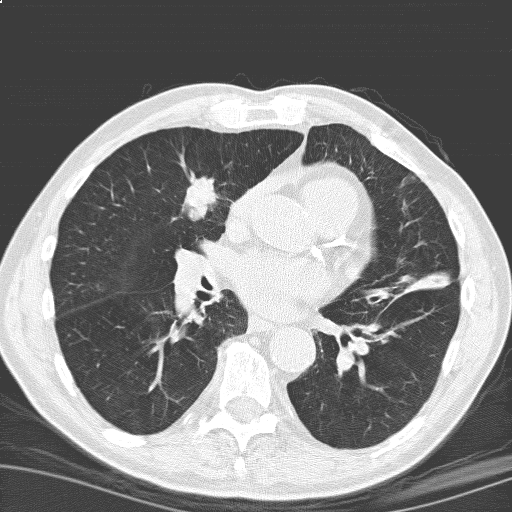
Low-dose screening chest CT, one axial slice; position 92 of 184 along the scan axis; 120 kVp; lung window (W 1500 / L -600 HU); 3.2 mm slice thickness; 512 × 512 image matrix.
Structures marked on this image (expert manual segmentation):
- lesion 1 (tumor, upper lobe of right lung): bounding box <184,177,217,219> (left, top, right, bottom; pixels)